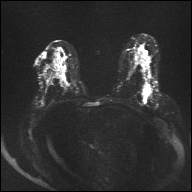
Breast MRI, one axial slice. Slice 19 of 32 in the series (ordered by position). Diffusion-weighted series; image 2 of 4 stored at this slice position (different b-values; order by instance number). 1.5 T. 4 mm slice thickness. 192 × 192 image matrix, field of view 360 × 360 mm. Female patient.
Structures marked on this image (manually delineated by an expert):
- tumour on diffusion-weighted imaging: box from (x=146, y=85) to (x=150, y=94) px